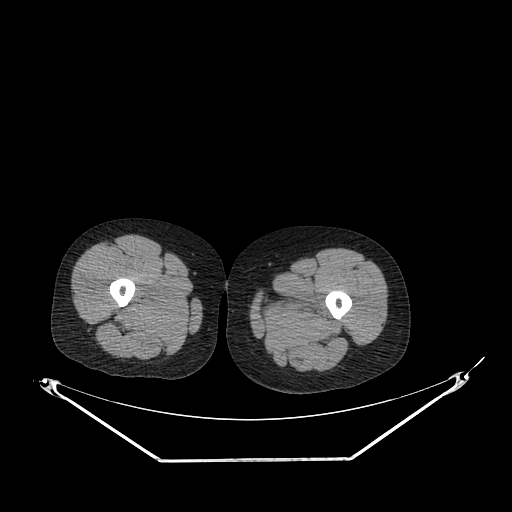
CT of an extremity soft-tissue mass (from a PET/CT study), one axial slice; position 223 of 267 along the scan axis; 120 kVp; soft-tissue window (W 400 / L 40 HU); 3.75 mm slice thickness; 512 × 512 image matrix, field of view 500 × 500 mm. Female patient. From the clinical record (not read from this slice): histological type: pleiomorphic leiomyosarcoma; grade: intermediate; site of the primary tumour: left thigh.
Structures marked on this image (expert contour drawn on MRI and transferred to this co-registered scan by the dataset authors):
- gross tumour volume including surrounding oedema: bounding box (x1, y1, x2, y2) in pixels: (262, 290, 325, 316)